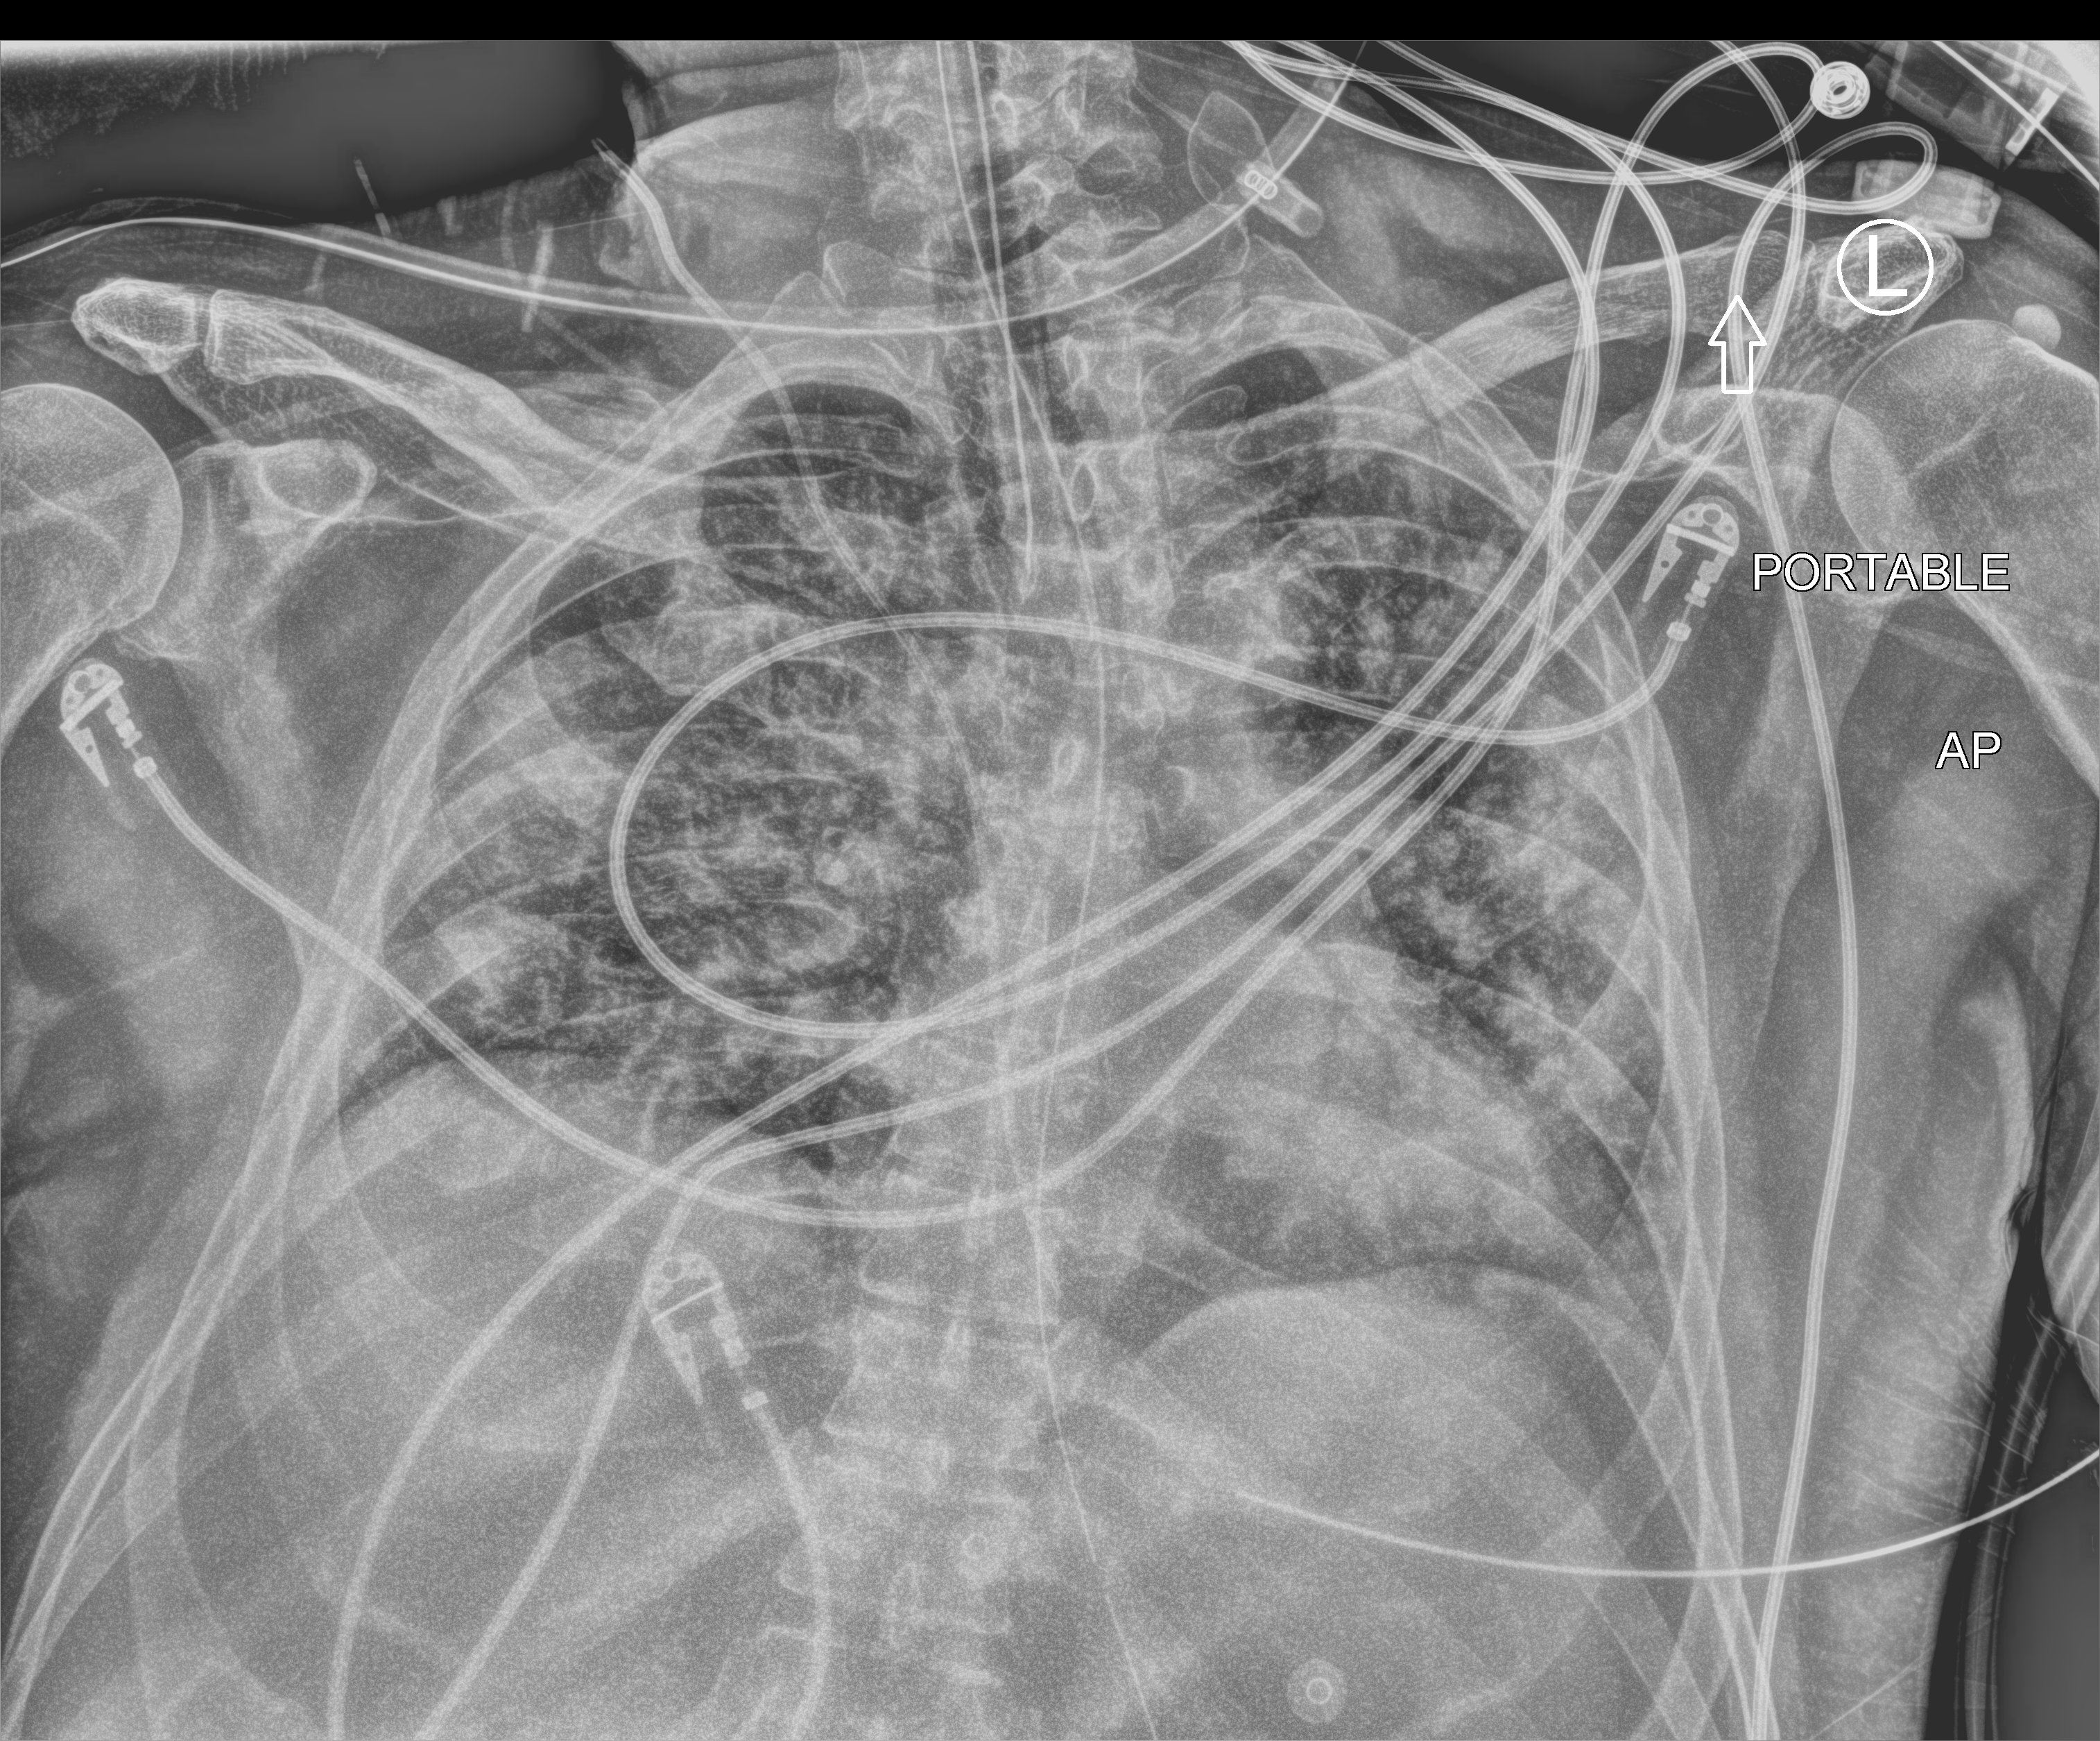
Portable chest radiograph; anteroposterior (AP) projection. Patient hospitalised with COVID-19; male, aged 18–59 years.
Admission-level facts for this patient (not findings on this image; timing relative to this image not recorded): admitted to intensive care during this hospital stay: yes.